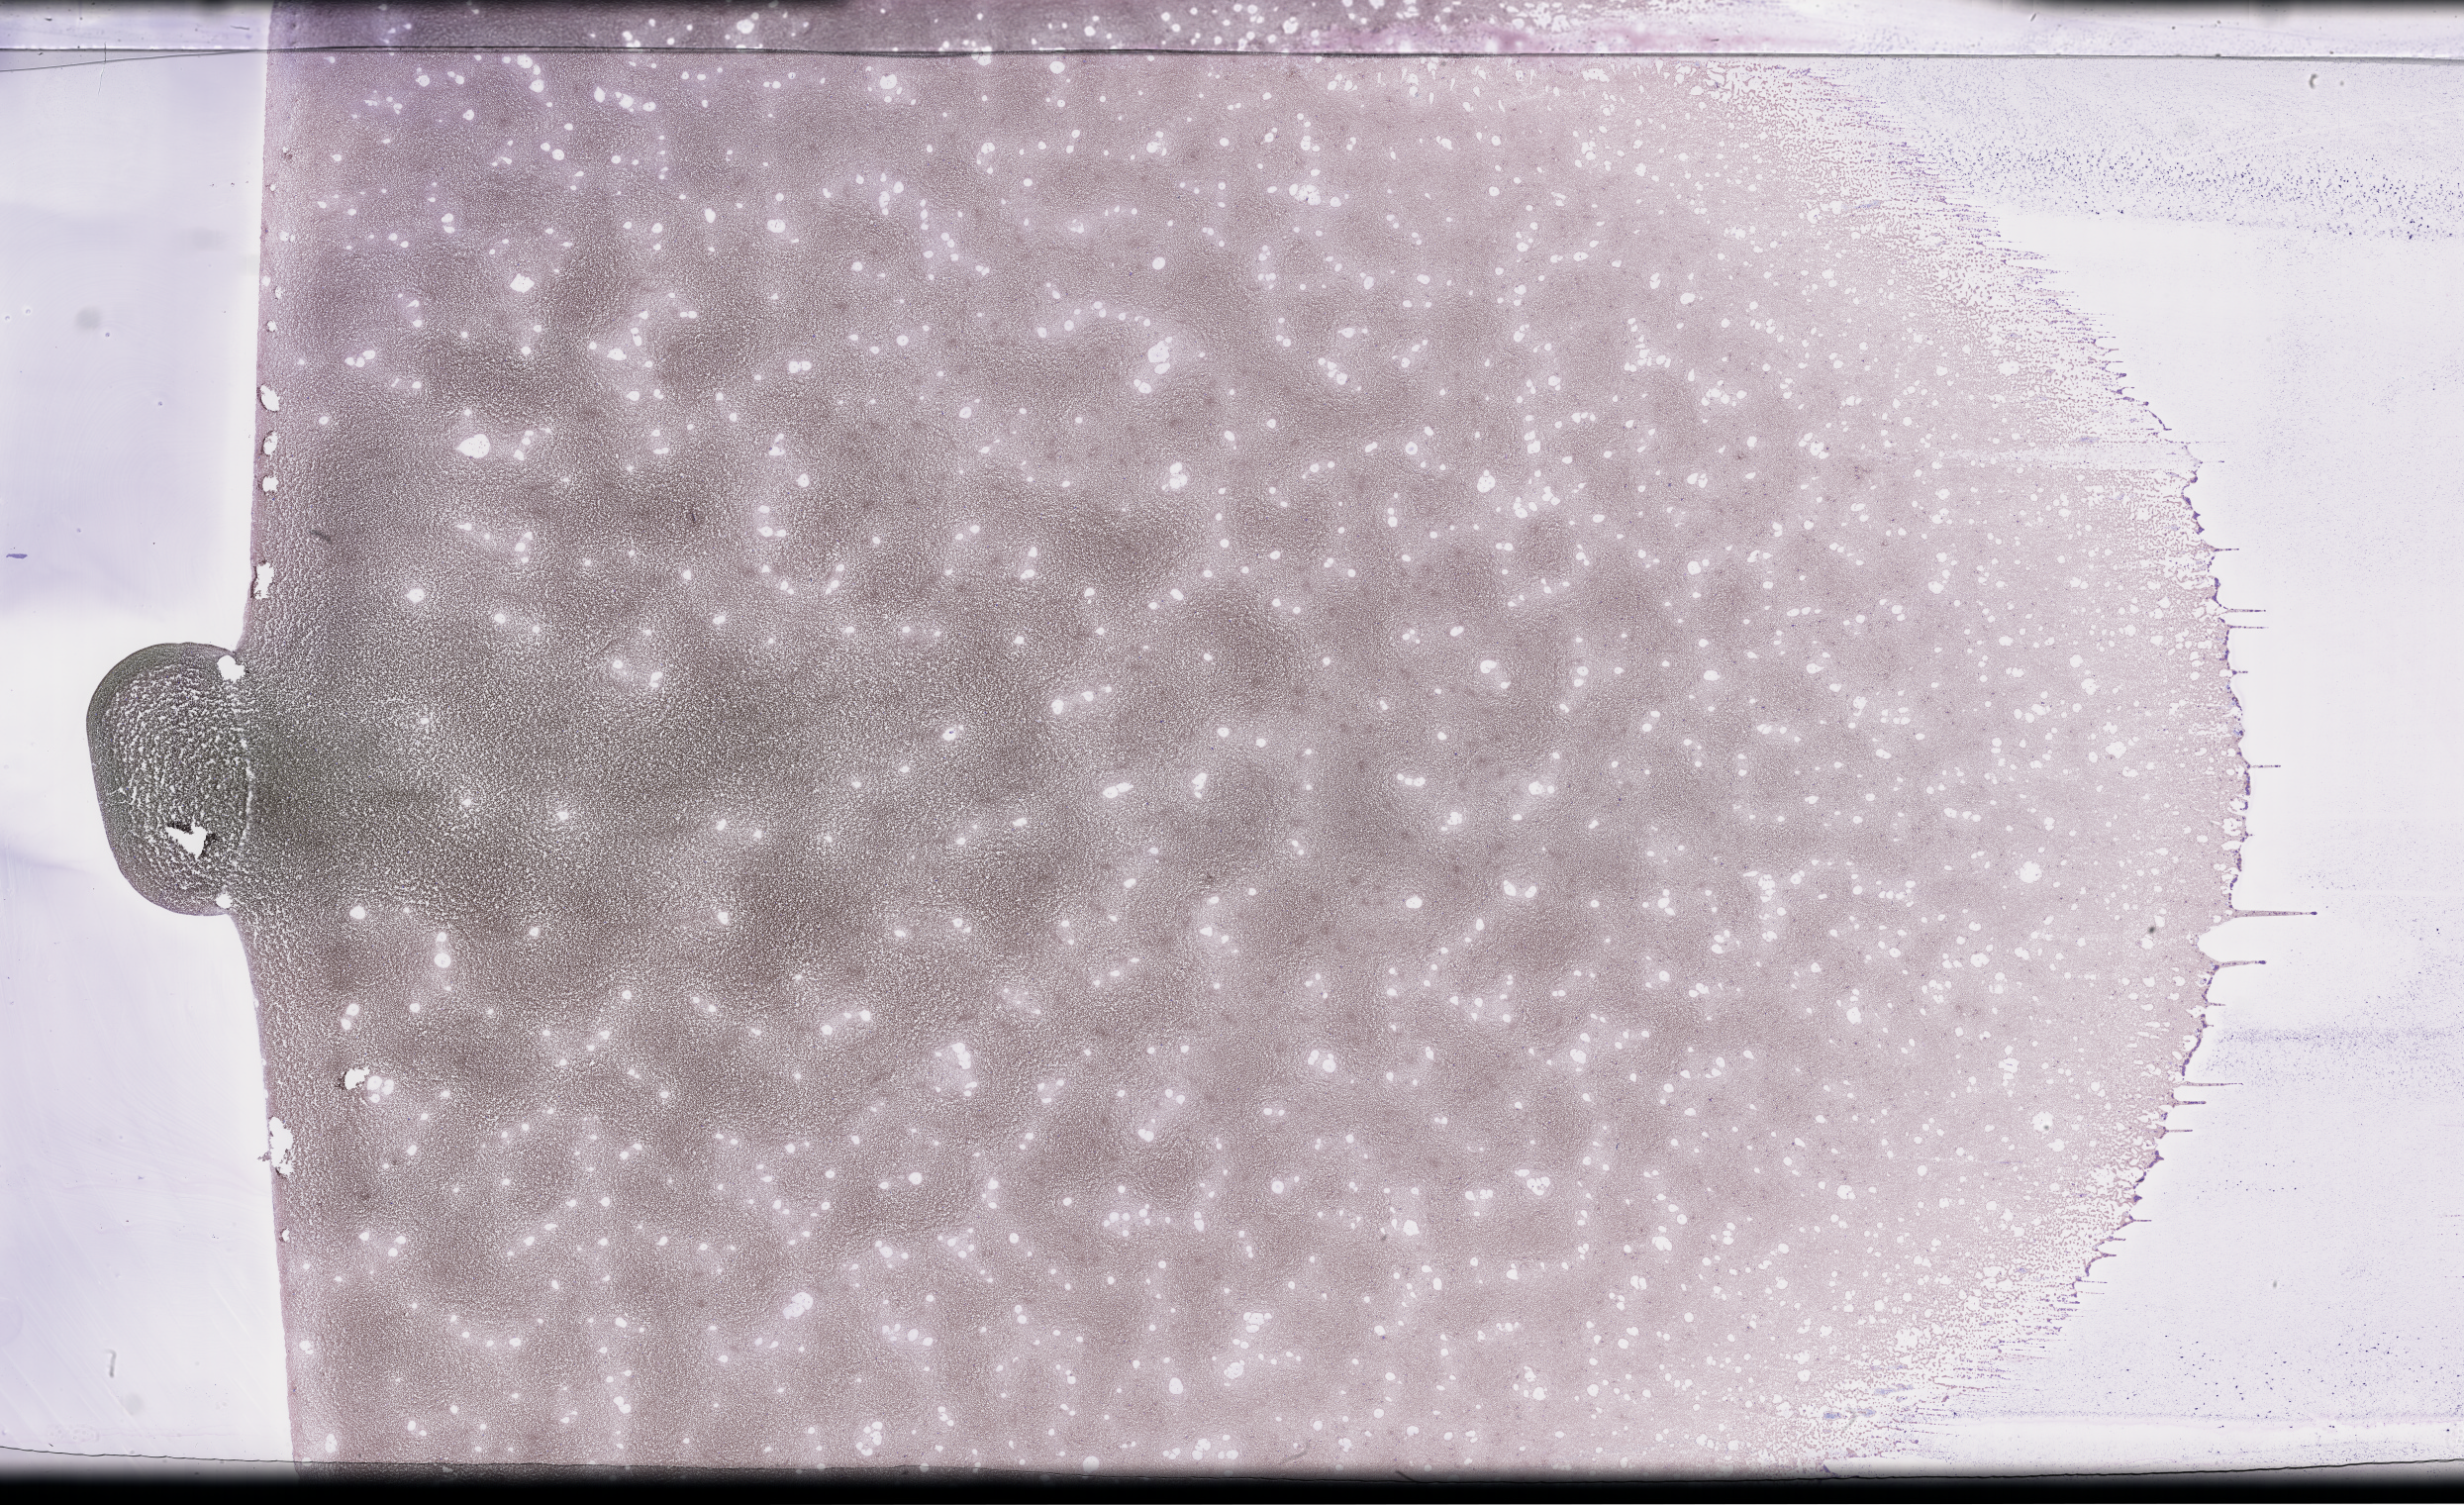
Whole-slide image of a whole blood smear, Wright-Giemsa stain, shown as a low-resolution overview of the whole scanned area (about 40.2 x 24.6 mm). Male patient.
Patient diagnosis: Plasma Cell Myeloma.